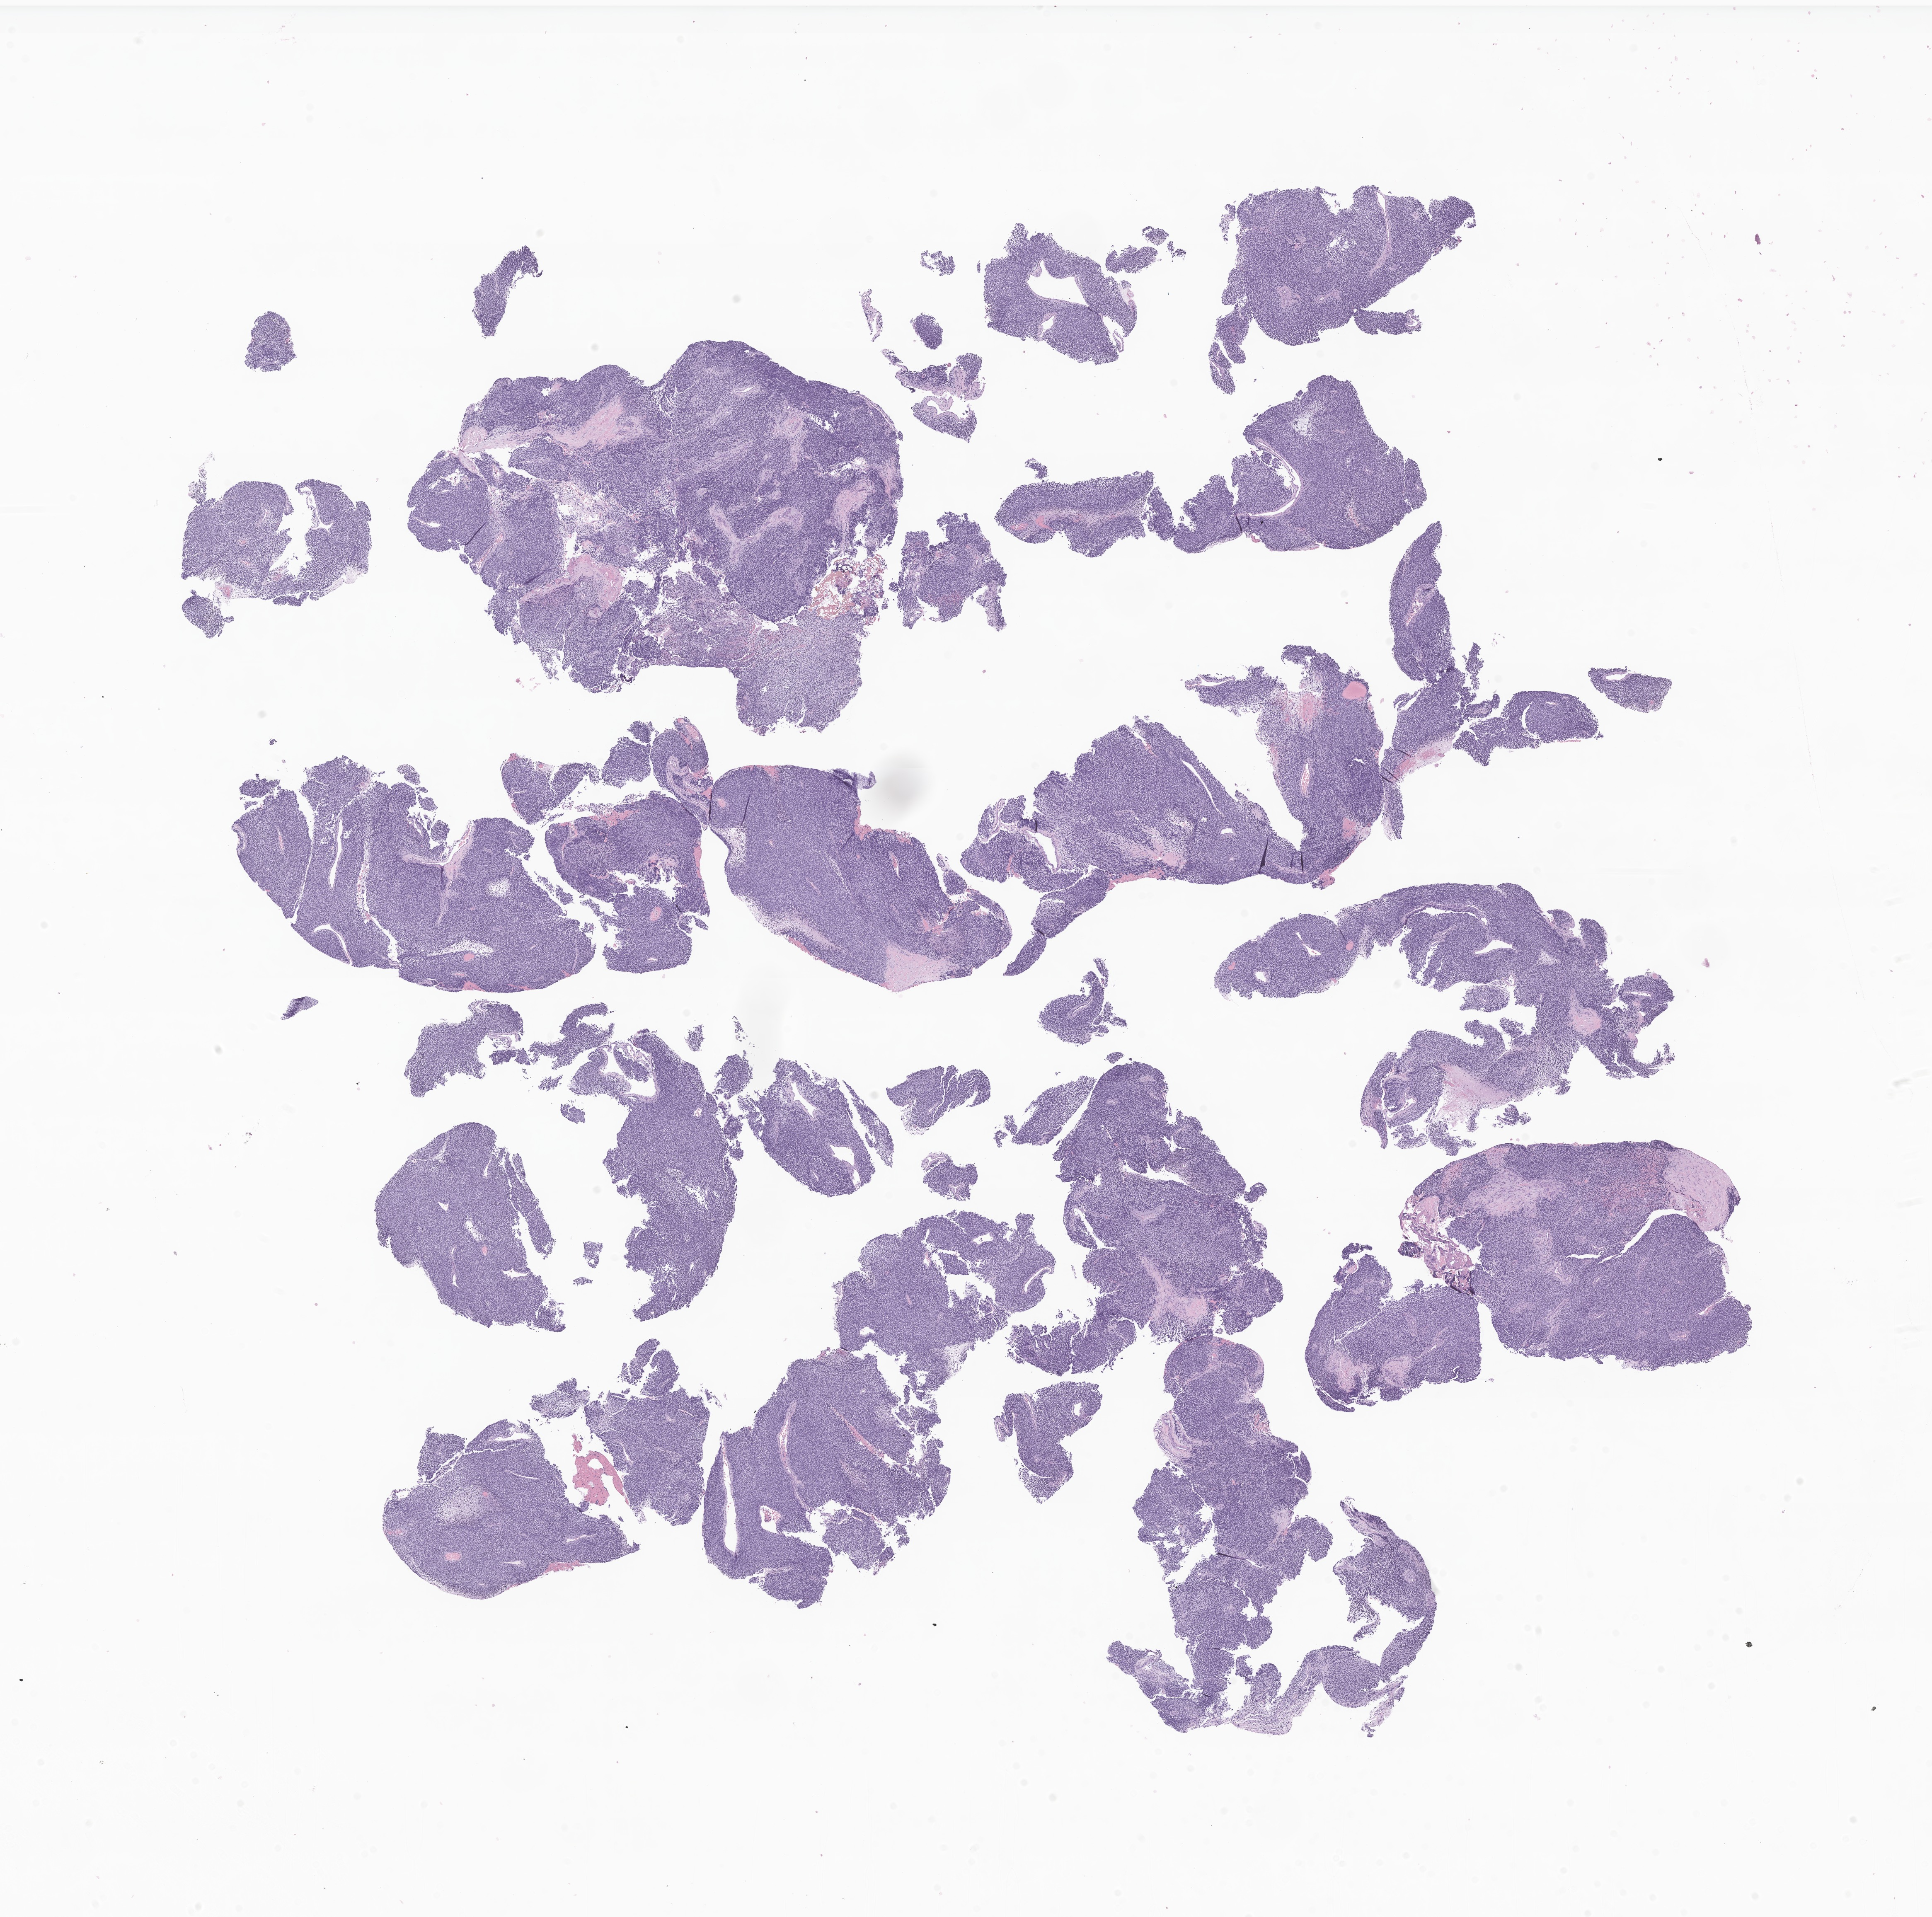
Digitized hematoxylin and eosin (H&E)-stained section of tumor tissue from the orbit — shown as a low-resolution overview of the whole scanned area (about 19.7 x 19.5 mm), formalin-fixed paraffin-embedded section. Patient: female, age 192 months (16 years).
Recorded diagnosis: Rhabdomyosarcoma, NOS.